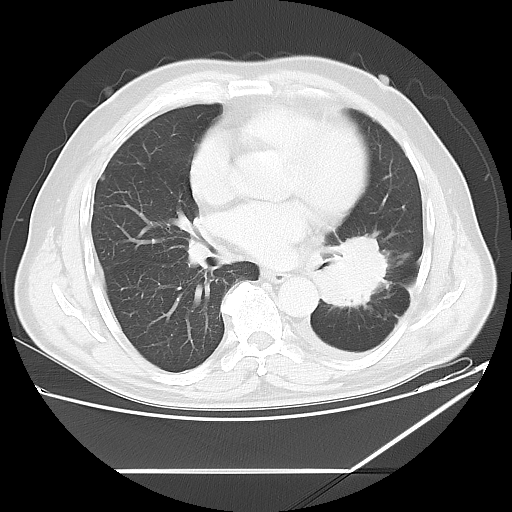
Chest CT, one axial slice. Position 29 of 60 along the scan axis. Reconstruction kernel LUNG. 120 kVp. Lung window (W 1500 / L -600 HU). 5 mm slice thickness. 512 × 512 image matrix, field of view 395 × 395 mm. Male patient, age 62 years. Case-level facts recorded for this patient, not image findings: clinical TNM (as recorded): T3 N0 M1.
Structures marked on this image (rectangle marked by the reading radiologist):
- lung tumour (recorded histology: adenocarcinoma): bounding box <315,230,393,315> (left, top, right, bottom; pixels)
- lung tumour (recorded histology: adenocarcinoma): <323,230,396,312>